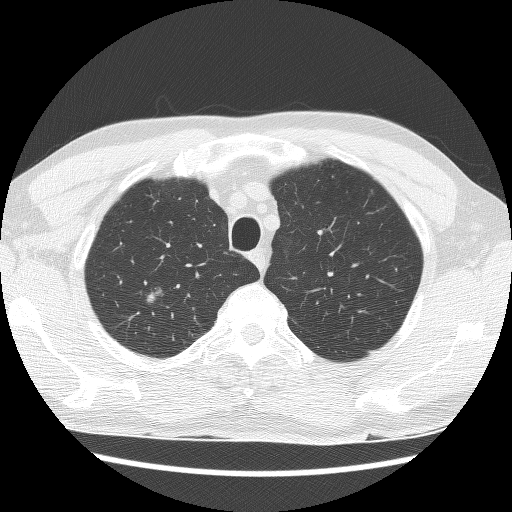
Low-dose screening chest CT, one axial slice; position 128 of 157 along the scan axis; reconstruction kernel BONE; 120 kVp; lung window (W 1500 / L -600 HU); 512 × 512 image matrix, field of view 340 × 340 mm.
Structures marked on this image (outlined manually by an expert reader):
- lesion 1 (tumor, upper lobe of right lung): box from (x=145, y=287) to (x=164, y=305) px